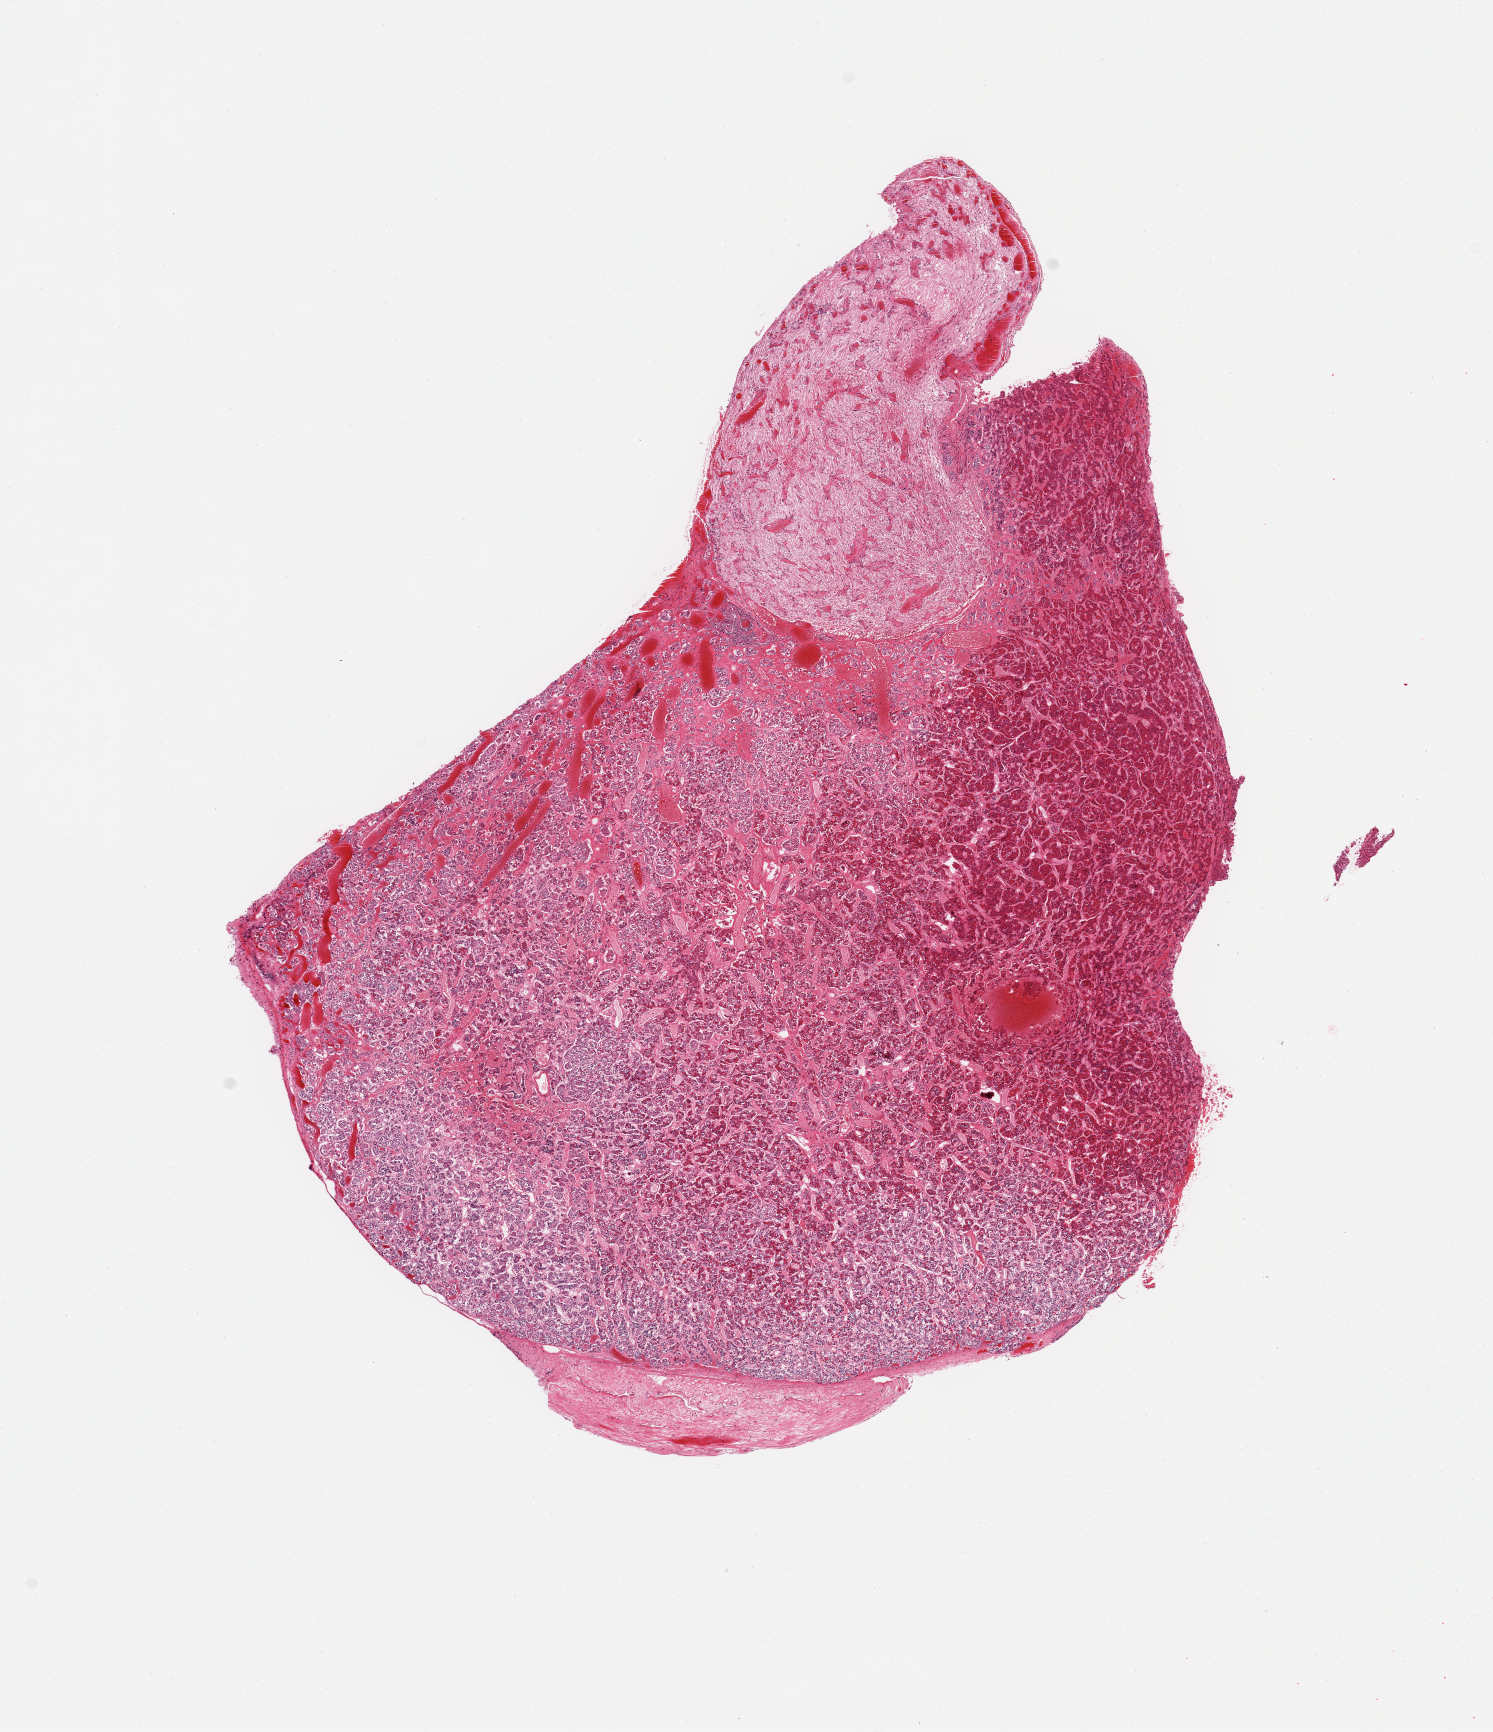
Whole-slide image, hematoxylin and eosin (H&E) stain, brightfield — shown as a low-resolution overview of the whole scanned area (about 11.8 x 13.7 mm, from a 20x scan), PAXgene-fixed, paraffin-embedded tissue, section of pituitary (target tissue), tissue donor sample. Male donor.
Review note (as recorded): 1 piece; adenohypophysis (80%) and neurohypophysis (20%); marked congestion.